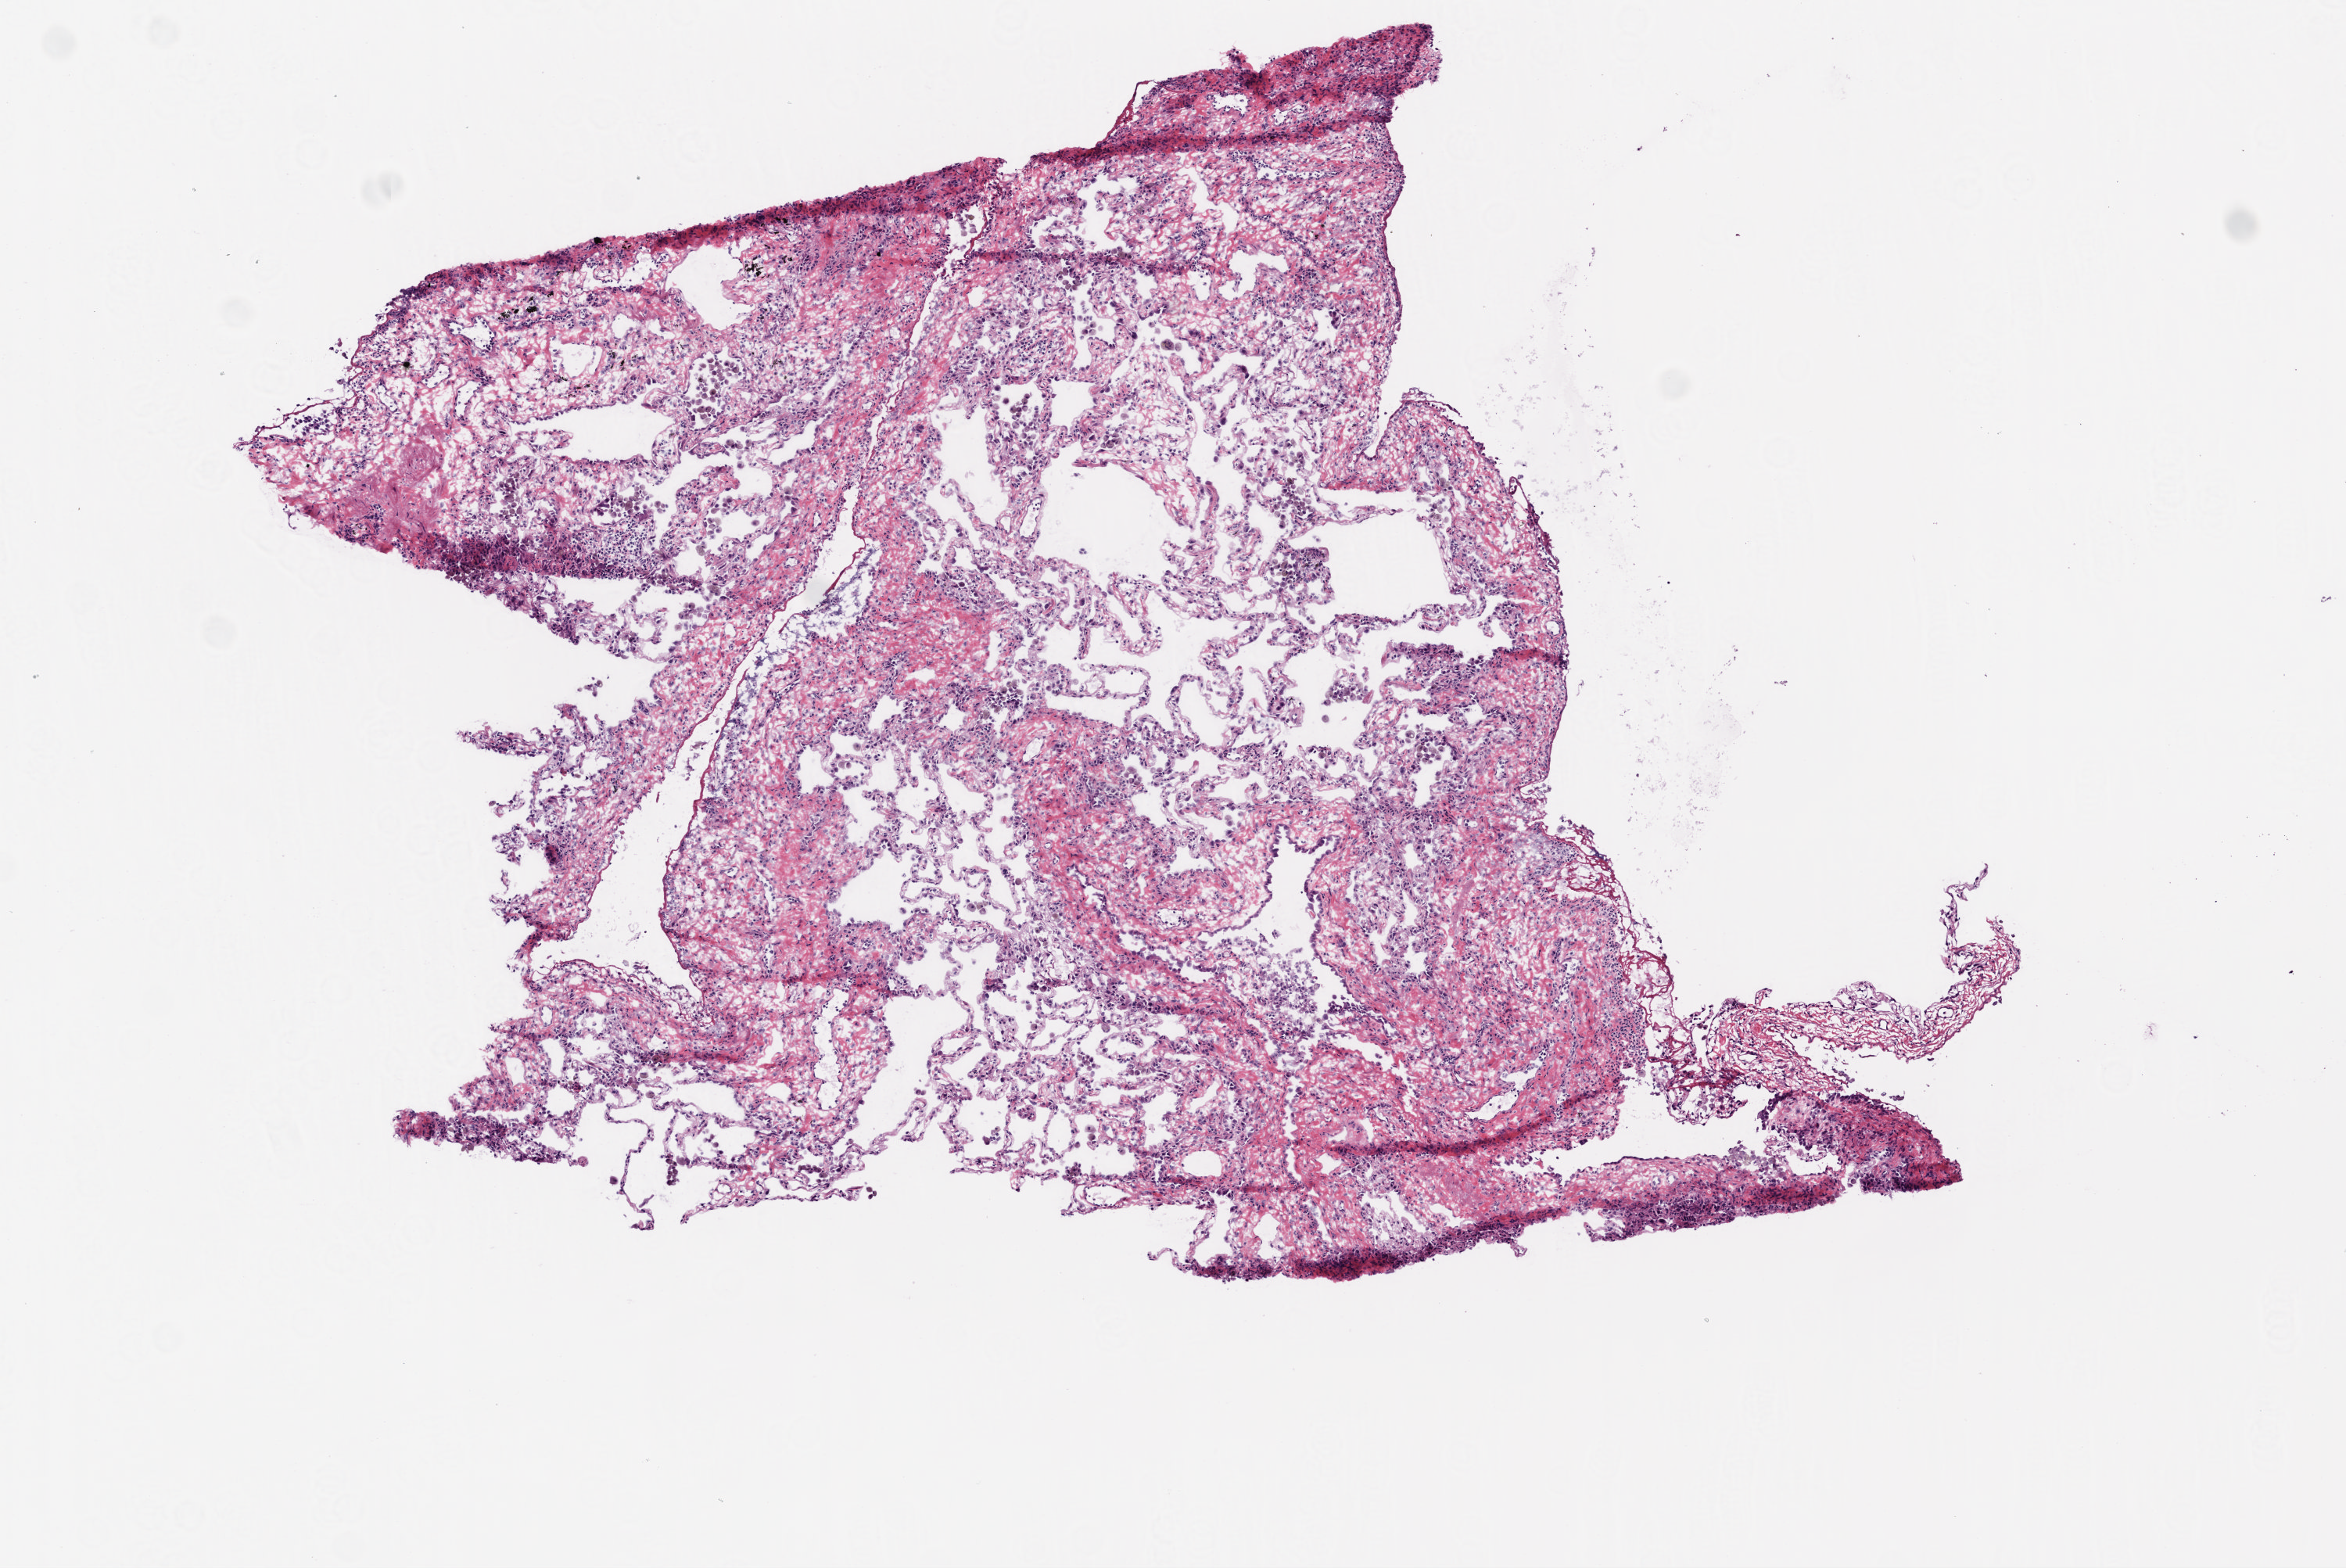
H&E-stained whole-slide image, whole scanned area (about 6.0 x 4.0 mm) shown as a low-resolution overview, frozen section, solid tissue normal (non-tumour tissue) sample from the lung. Male, age 77 years at initial diagnosis.
This section: solid tissue normal sample (biorepository sample class). Patient diagnosis: Squamous cell carcinoma, NOS.